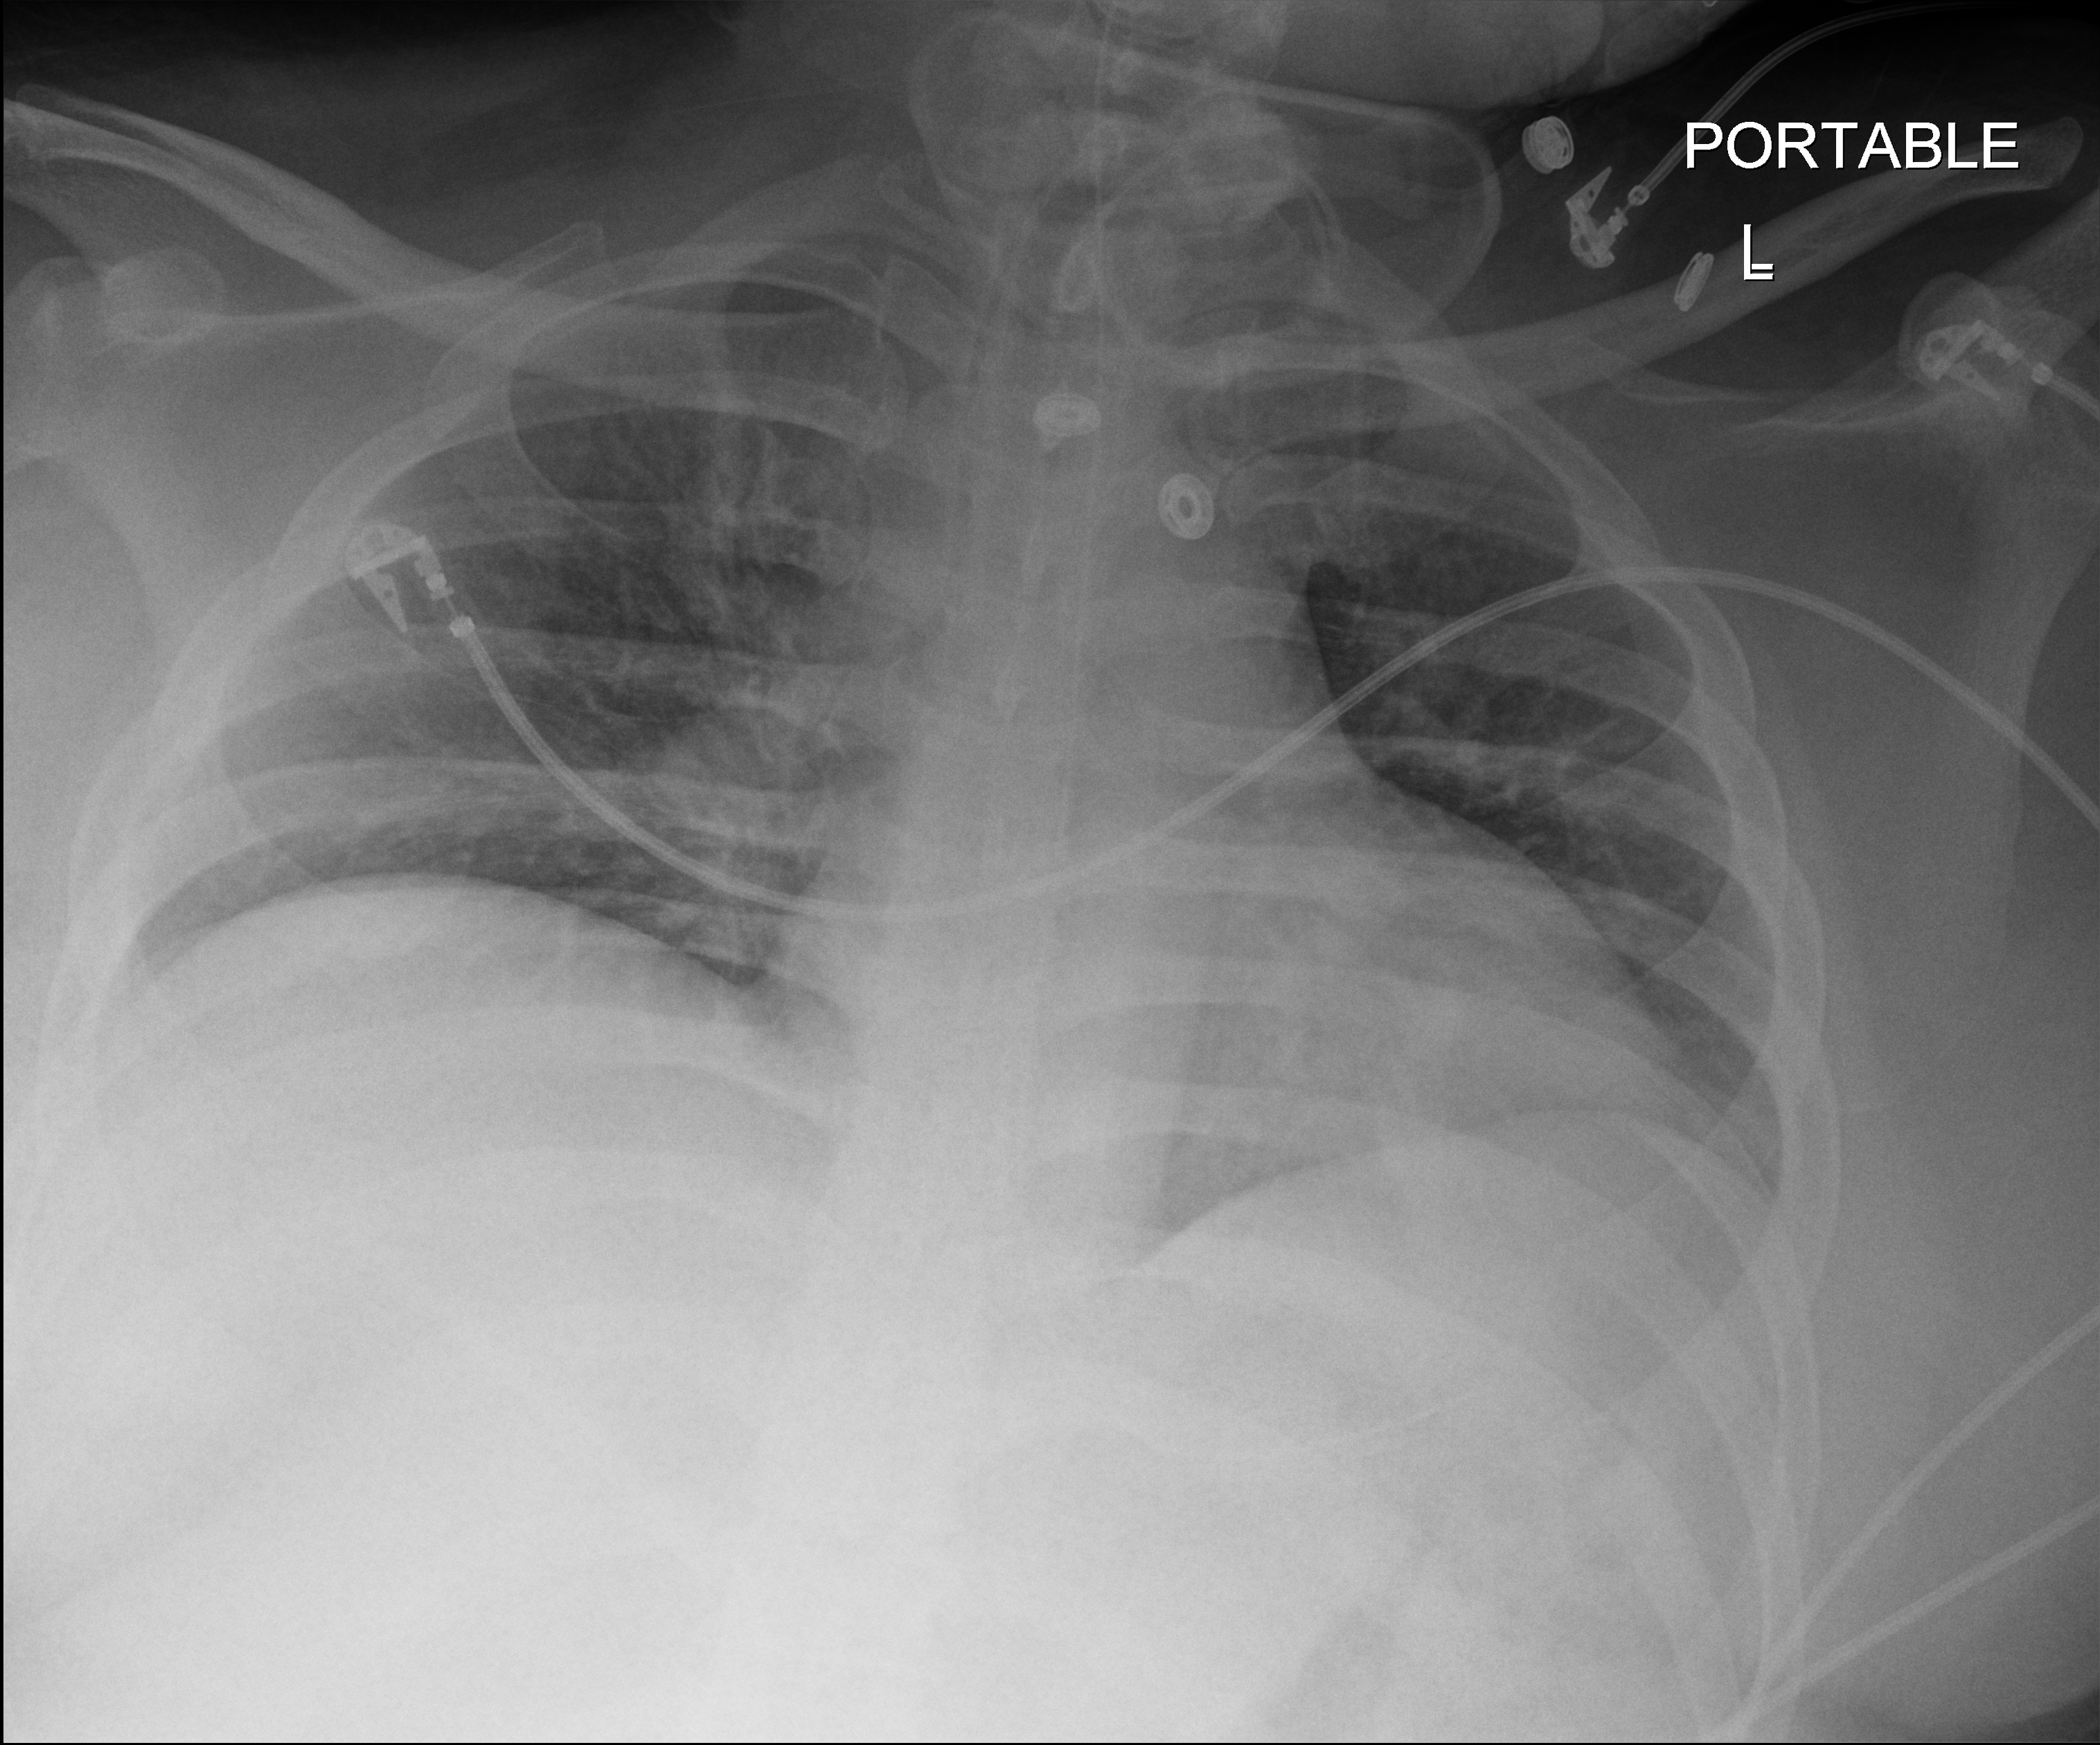
Bedside chest radiograph (digital radiography), anteroposterior (AP) projection. Patient hospitalised with COVID-19; male, aged 18–59 years.
Admission-level facts for this patient (not findings on this image; timing relative to this image not recorded): mechanically ventilated during this hospital stay: yes.